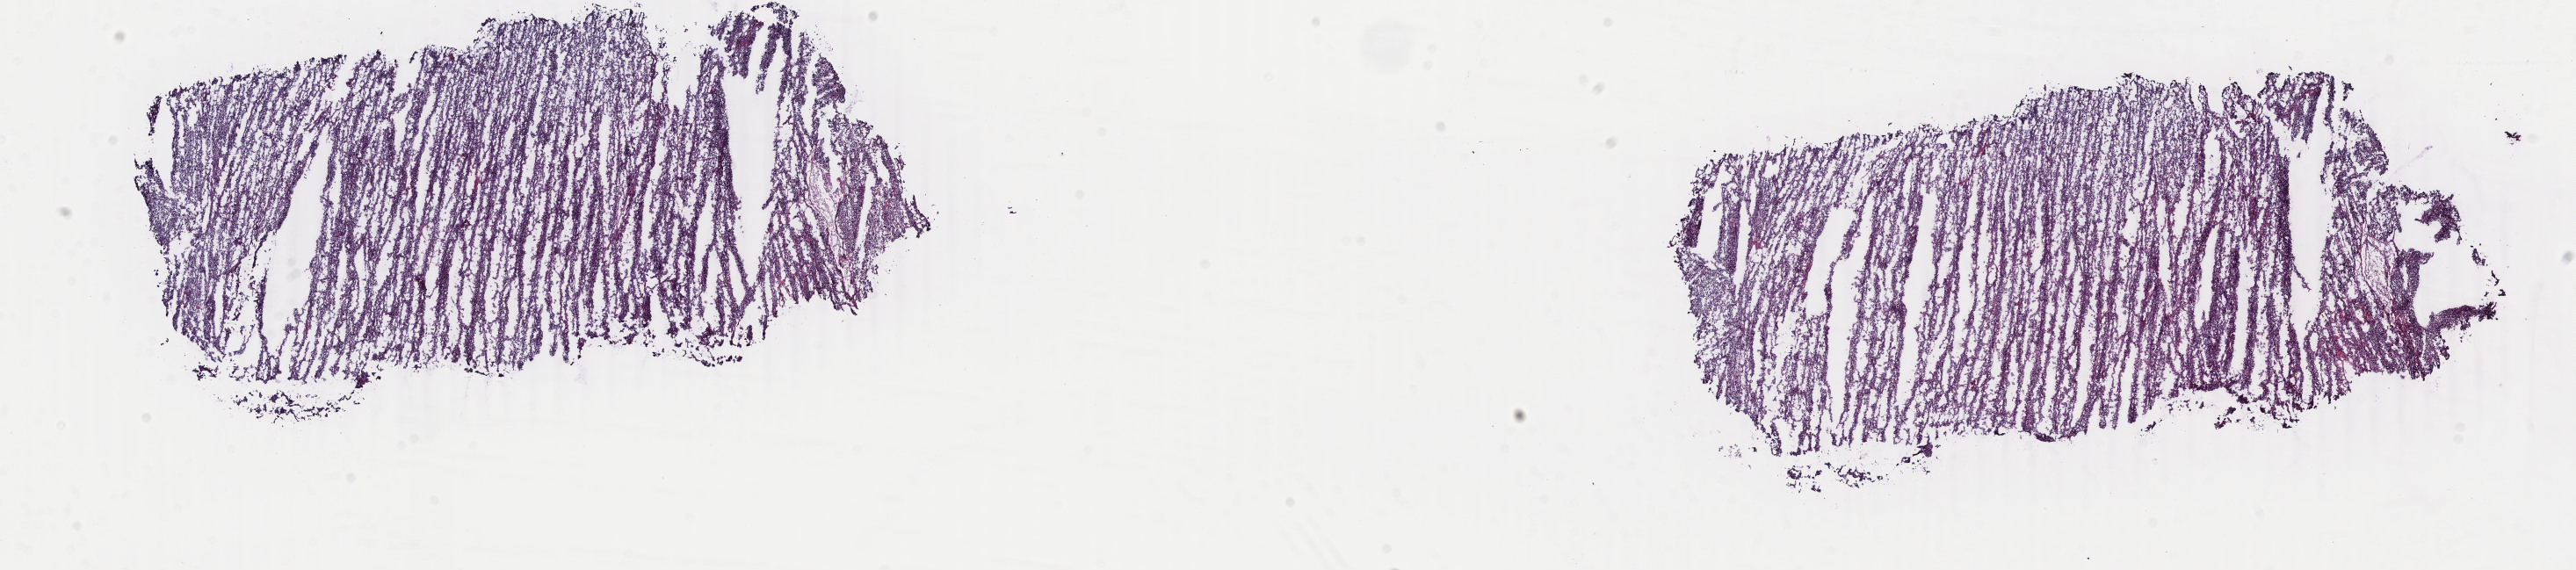
H&E-stained whole-slide image, low-resolution overview of the scanned area, about 23.3 x 5.2 mm, frozen section, uterus, primary tumour sample. Female, age 62 years at initial diagnosis. Composition of this section per pathologist review: tumour cells 100%, tumour nuclei 80%, normal cells 0%, stromal cells 0%, necrosis 0%. Infiltration values recorded for this section: lymphocyte infiltration 1%, monocyte infiltration 0%, neutrophil infiltration 0%.
Histologic diagnosis: Mullerian mixed tumor. Lymph nodes positive (case pathology): 0 of 10 examined. FIGO stage: IA.